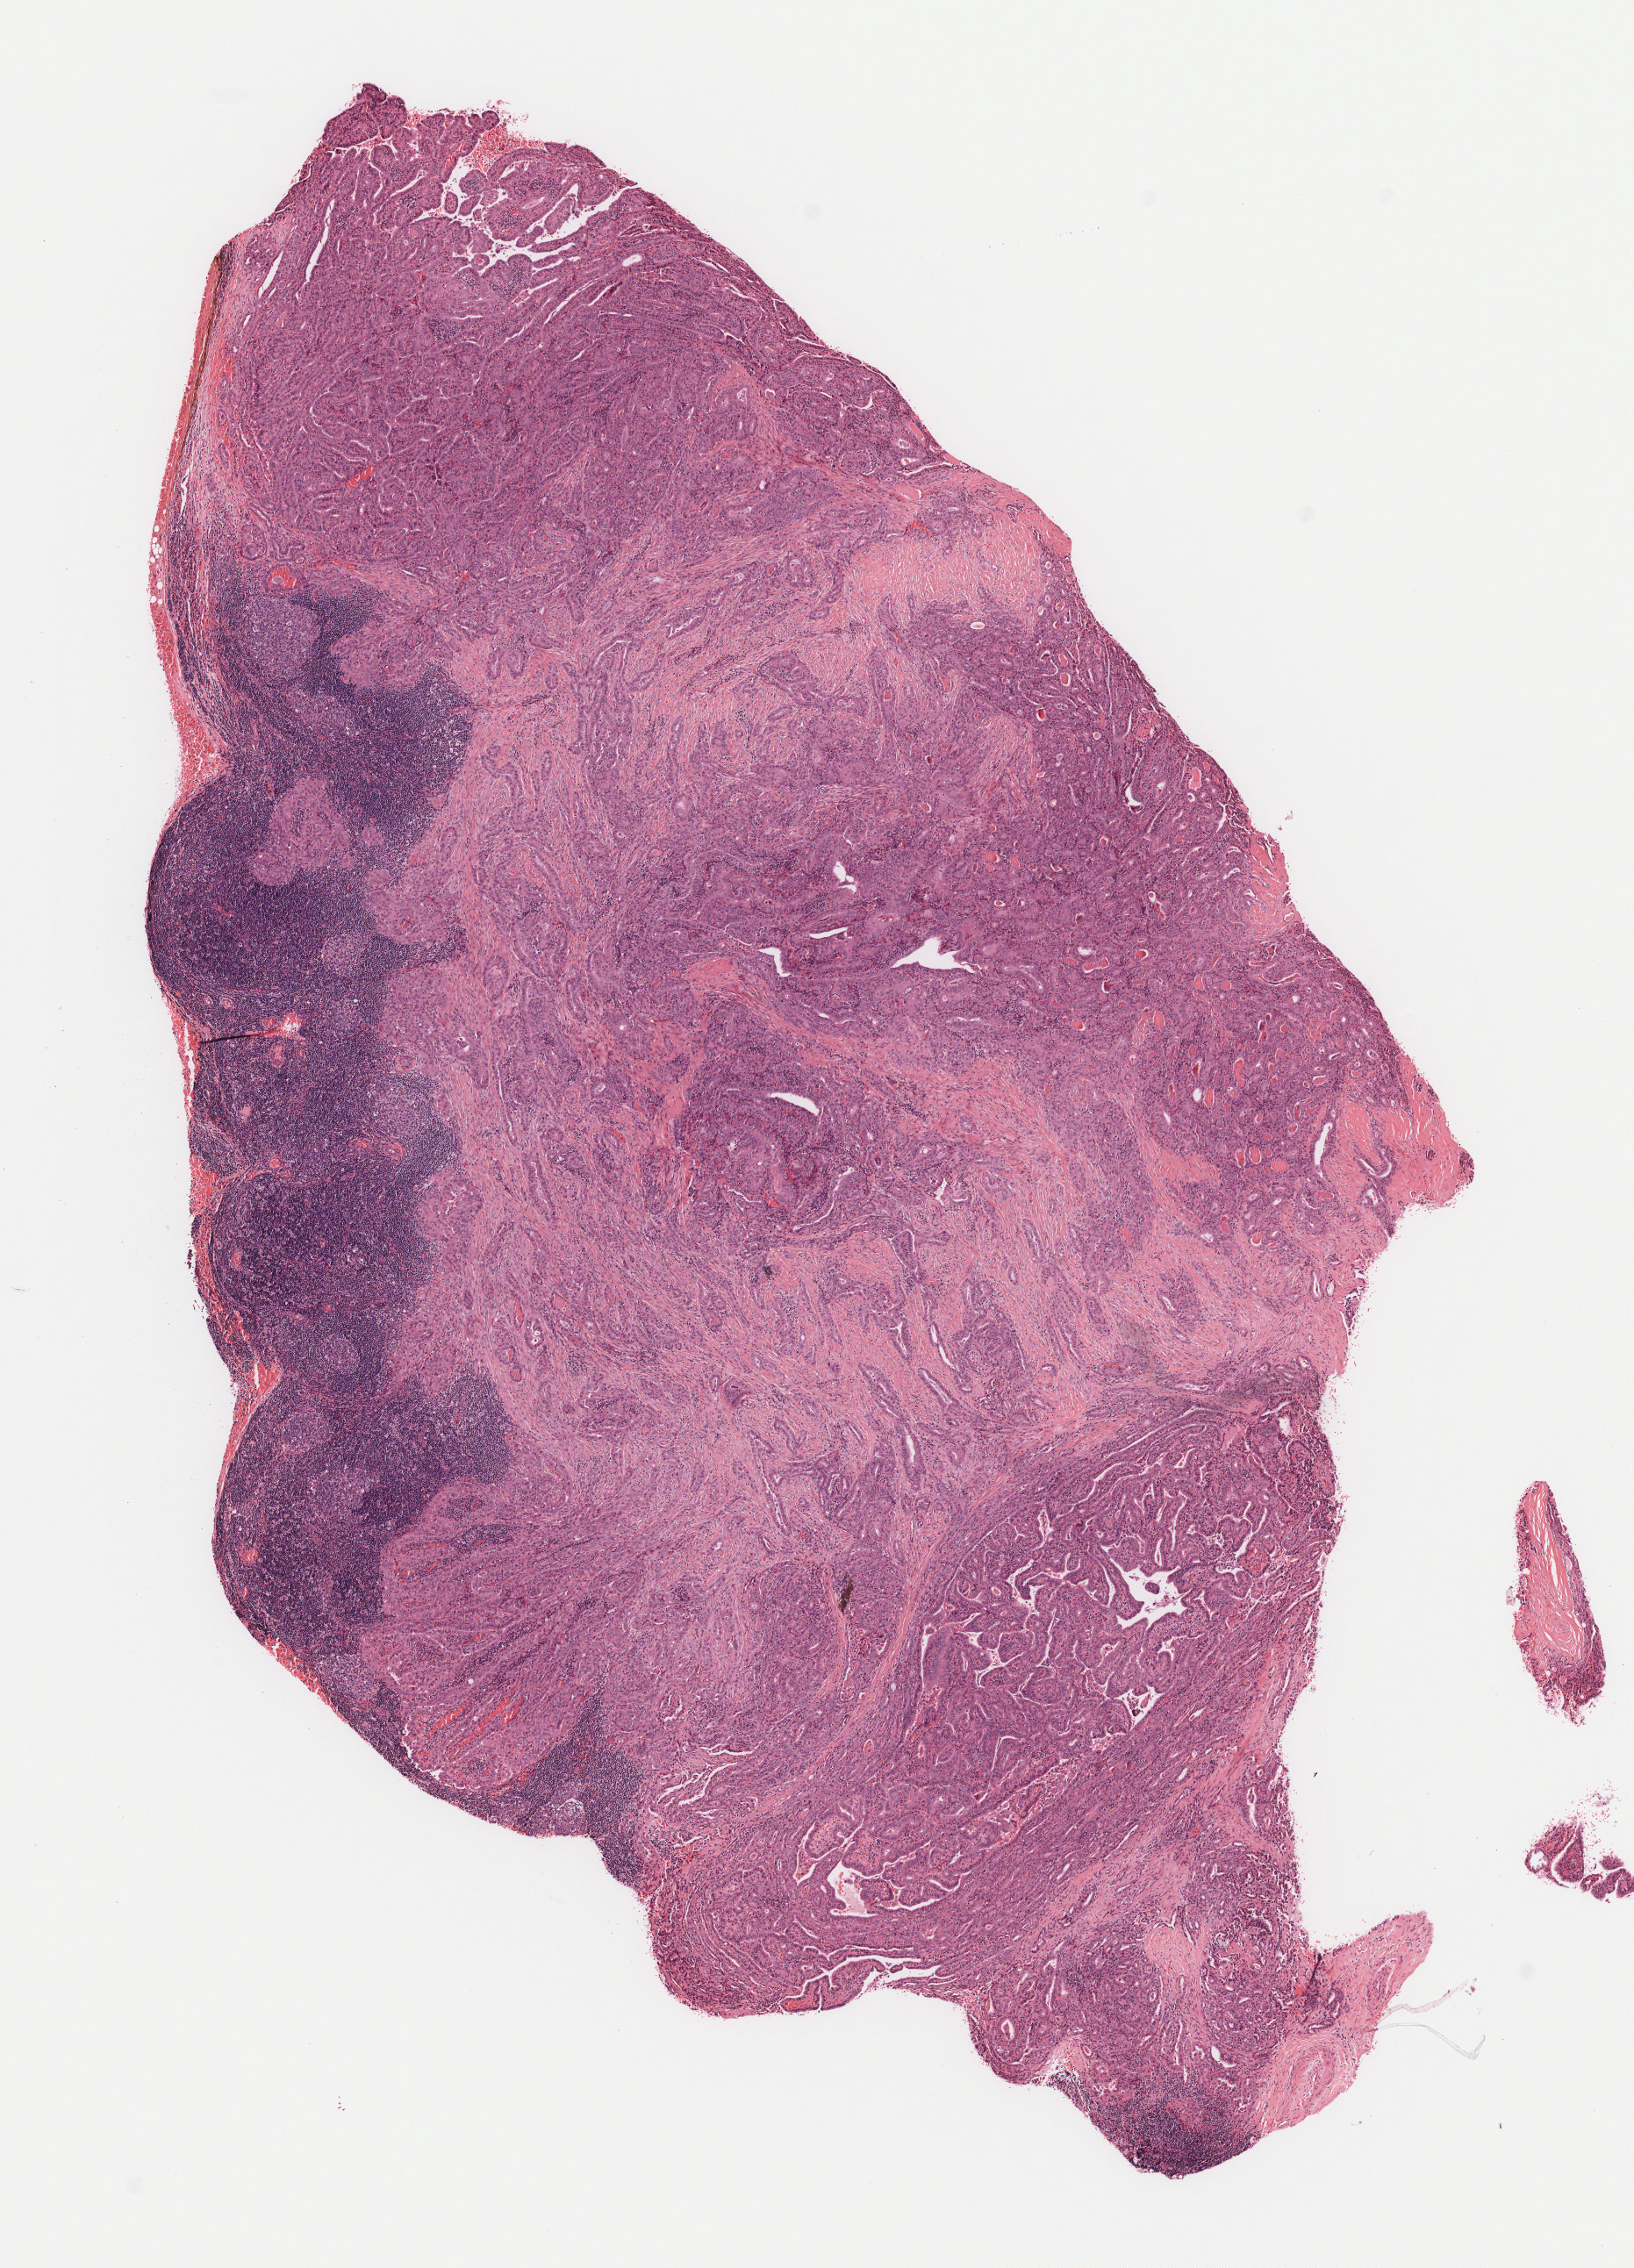
Whole-slide histology image, Hematoxylin and eosin (H&E) stained — shown as a low-resolution overview of the whole scanned area (about 7.5 x 10.4 mm, slide scanned at 40x). Formalin-fixed paraffin-embedded (FFPE) diagnostic section. Thyroid, primary tumour sample. Patient: male, age at initial diagnosis 33 years.
* pathologic diagnosis: Papillary adenocarcinoma, NOS (thyroid gland)
* lymph nodes positive (case pathology): 15 of 54 examined
* AJCC pathologic stage: I (7th edition)
* TNM: T2 N1b MX
* laterality: left